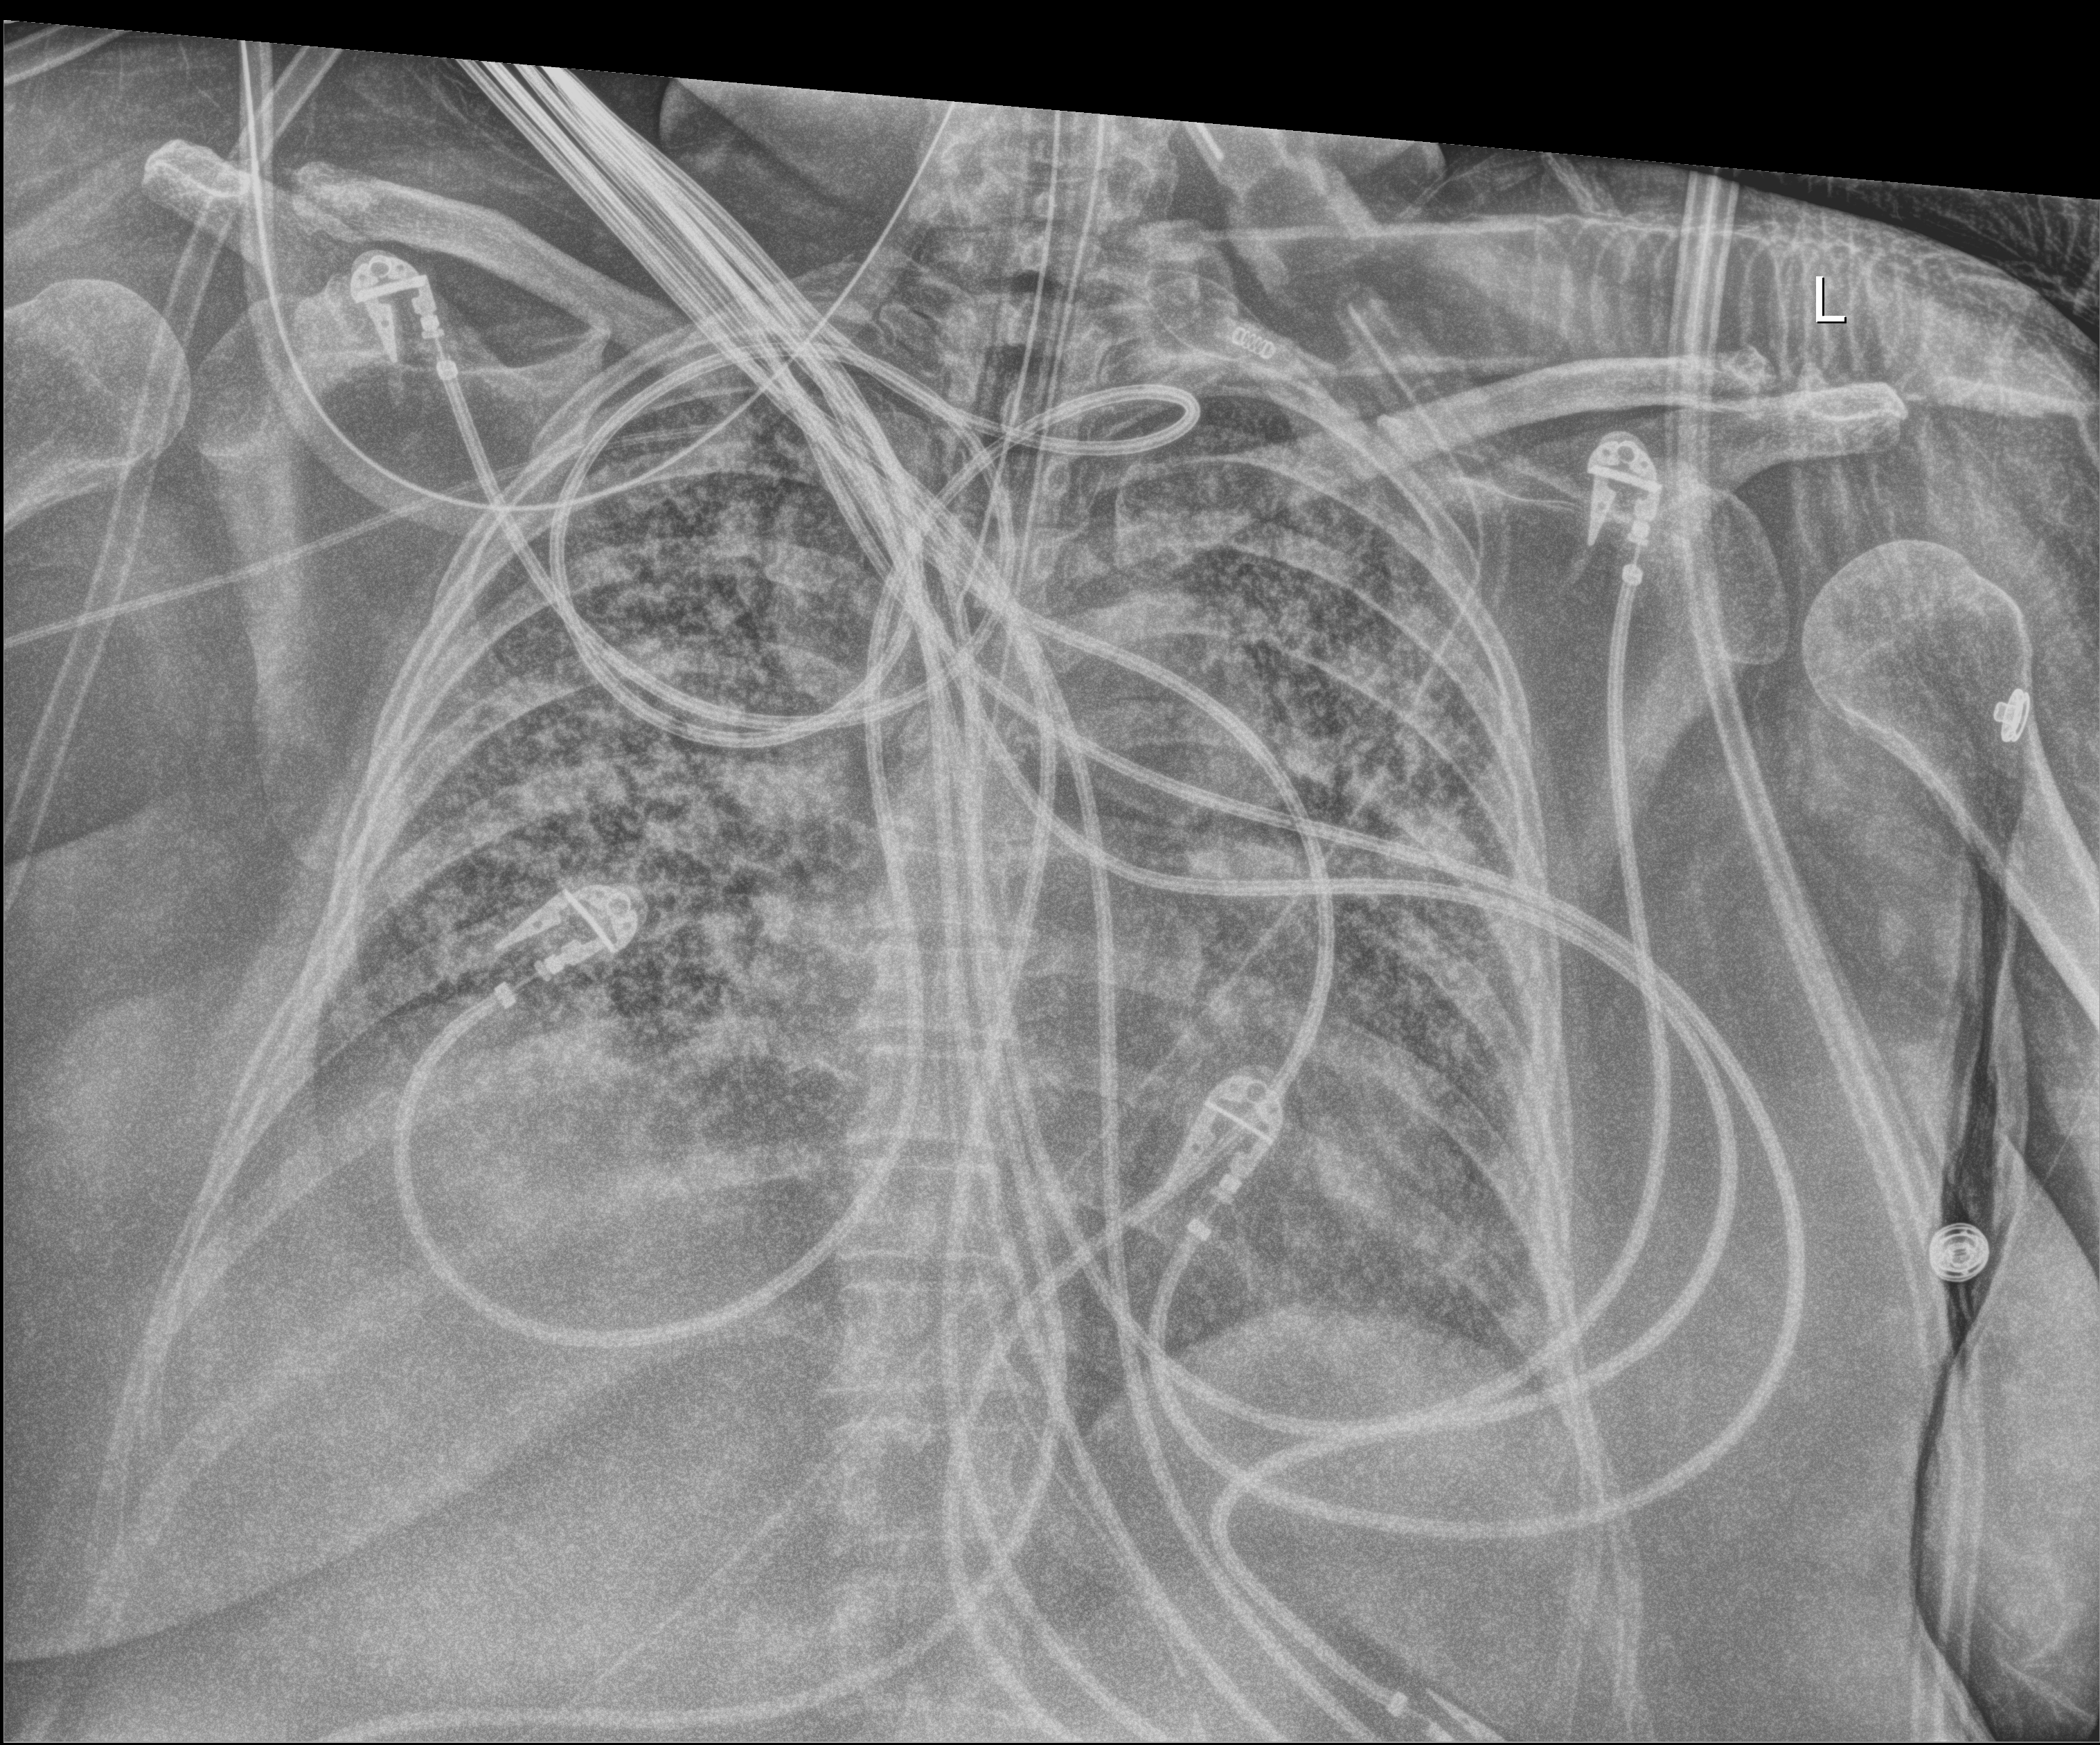
Chest radiograph (digital radiography). Patient hospitalised with COVID-19; female, aged 18–59 years.
Admission-level facts for this patient (not findings on this image; timing relative to this image not recorded): mechanically ventilated during this hospital stay: yes; other chronic lung disease (admission record): no; length of hospital stay: 95 days.